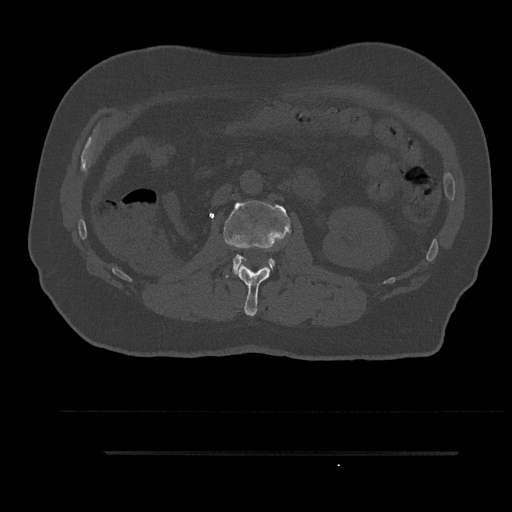
CT including the spine, one axial slice. Position 140 of 797 along the scan axis. Reconstruction kernel Br40s/3. Bone window (W 1800 / L 400 HU). 512 × 512 image matrix. Male patient, age 63 years. Case-level facts recorded for this patient, not image findings: primary cancer: renal; vertebrae with lytic lesions (as recorded): T8.
Structures marked on this image (semi-automatically segmented with operator editing):
- L1 vertebra: bounding box (x1, y1, x2, y2) in pixels: (236, 264, 272, 316)
- L2 vertebra: (223, 201, 291, 274)